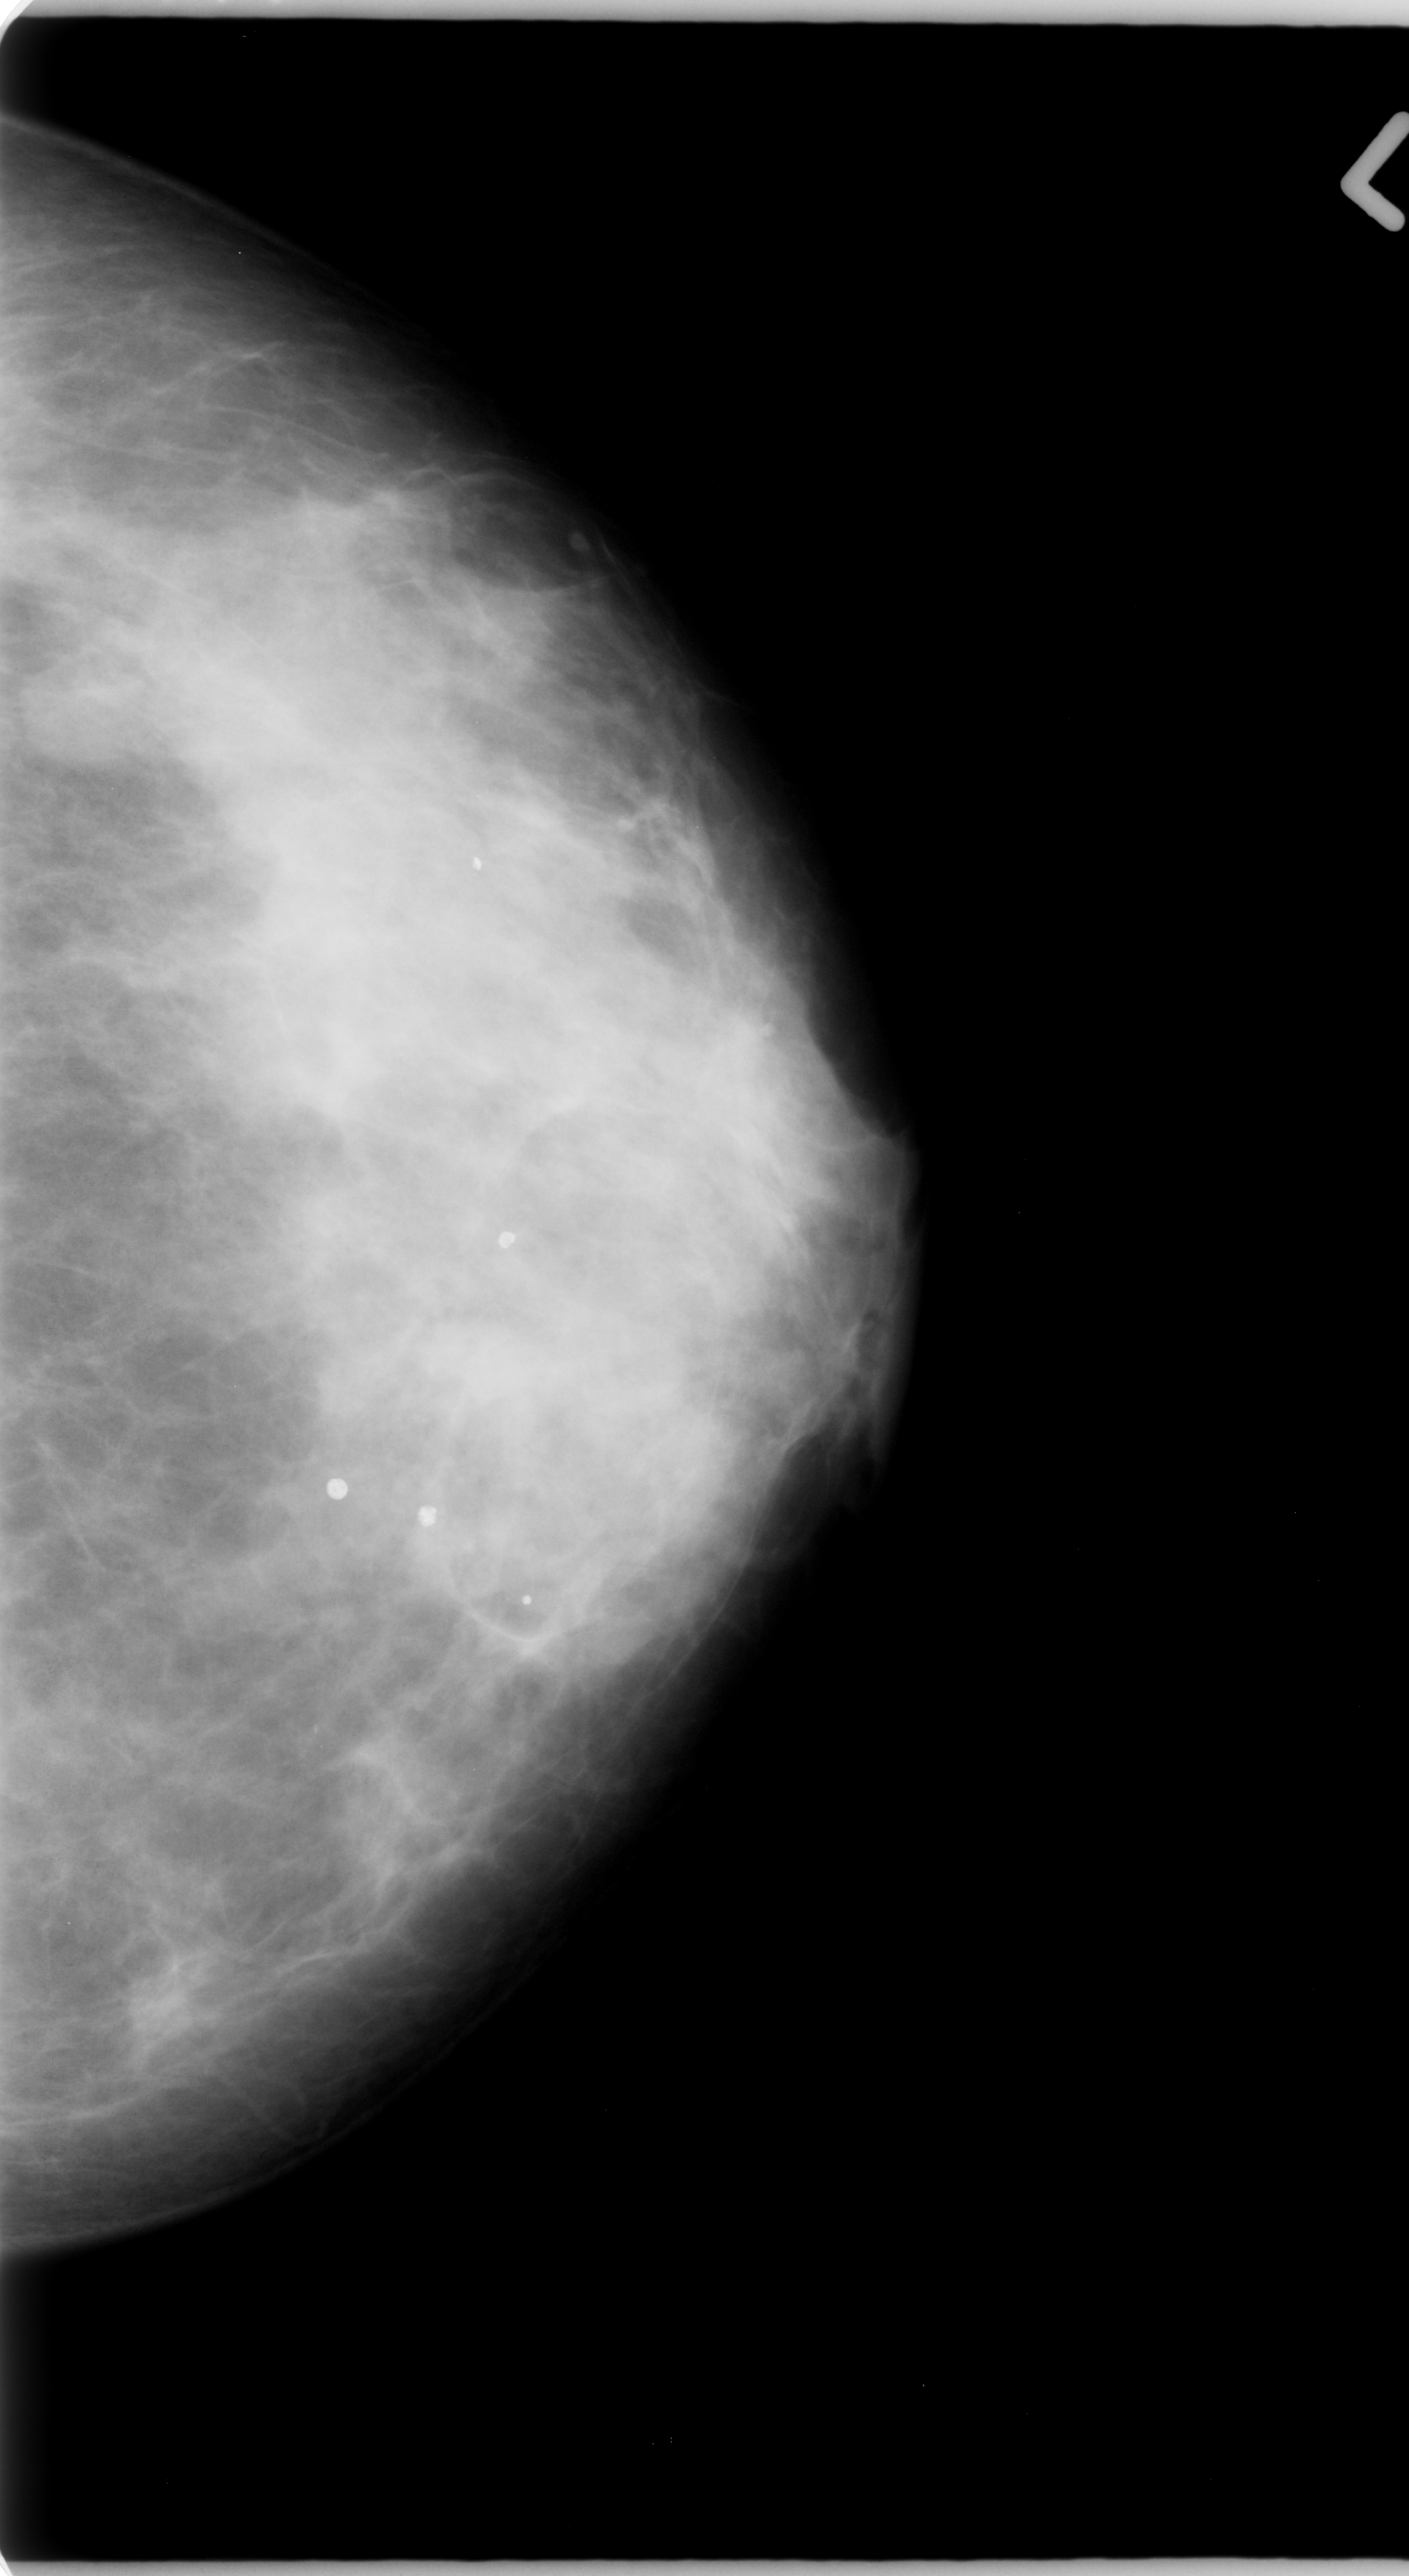
Scanned film-screen mammogram; left breast; CC view.
Marked abnormality: mass, shape oval, margins microlobulated; BI-RADS assessment category 4; pathology result (as recorded, not read from the image): malignant.